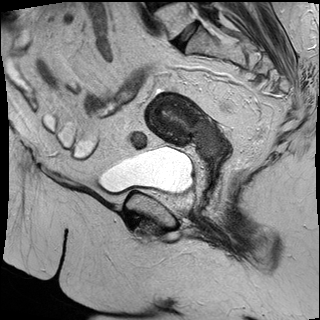
Pelvic MRI for cervical cancer, one sagittal slice; slice 15 of 32 in the series (ordered by position); T2-weighted; 1.5 T; TE 87 ms, TR 3063.4 ms; 4 mm slice thickness; 320 × 320 image matrix, field of view 280 × 280 mm. Female patient, age 53 years.
Annotated regions visible in this slice (outlined manually by an expert reader):
- uterus and cervix: bounding box [x1, y1, x2, y2] px = [146, 93, 229, 161]